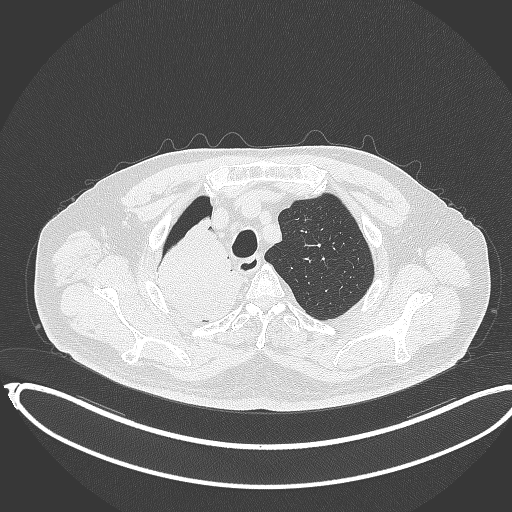
Chest CT, one axial slice; slice 308 of 403 in the series (ordered by position); reconstruction kernel B70f; lung window (W 1500 / L -600 HU); 1 mm slice thickness; 512 × 512 image matrix. Male patient, age 68 years. From the clinical record (not read from this slice): clinical TNM (as recorded): T2a N0 M0.
Structures marked on this image (rectangle marked by the reading radiologist):
- lung tumour (recorded histology: adenocarcinoma): bounding box <150,218,250,327> (left, top, right, bottom; pixels)